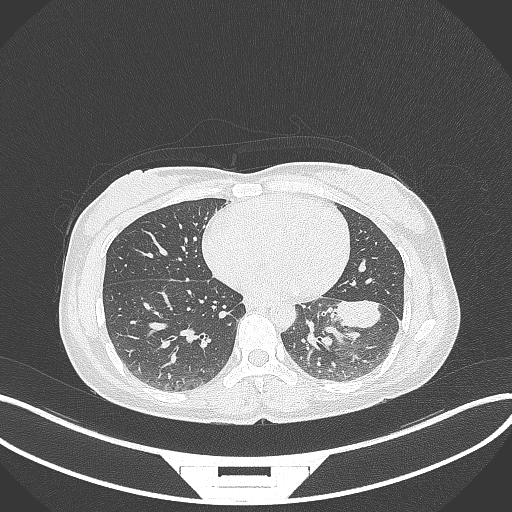
Chest CT, one axial slice. Slice 25 of 244 in the series (ordered by position). Reconstruction kernel B70f. 120 kVp. Lung window (W 1500 / L -600 HU). 1 mm slice thickness. 512 × 512 image matrix, field of view 400 × 400 mm. Female patient, age 41 years. Case-level facts recorded for this patient, not image findings: clinical TNM (as recorded): T2a N3 M1b.
Outlined on this slice (bounding box drawn by a radiologist):
- lung tumour (recorded histology: adenocarcinoma): bounding box (x1, y1, x2, y2) in pixels: (335, 296, 388, 332)